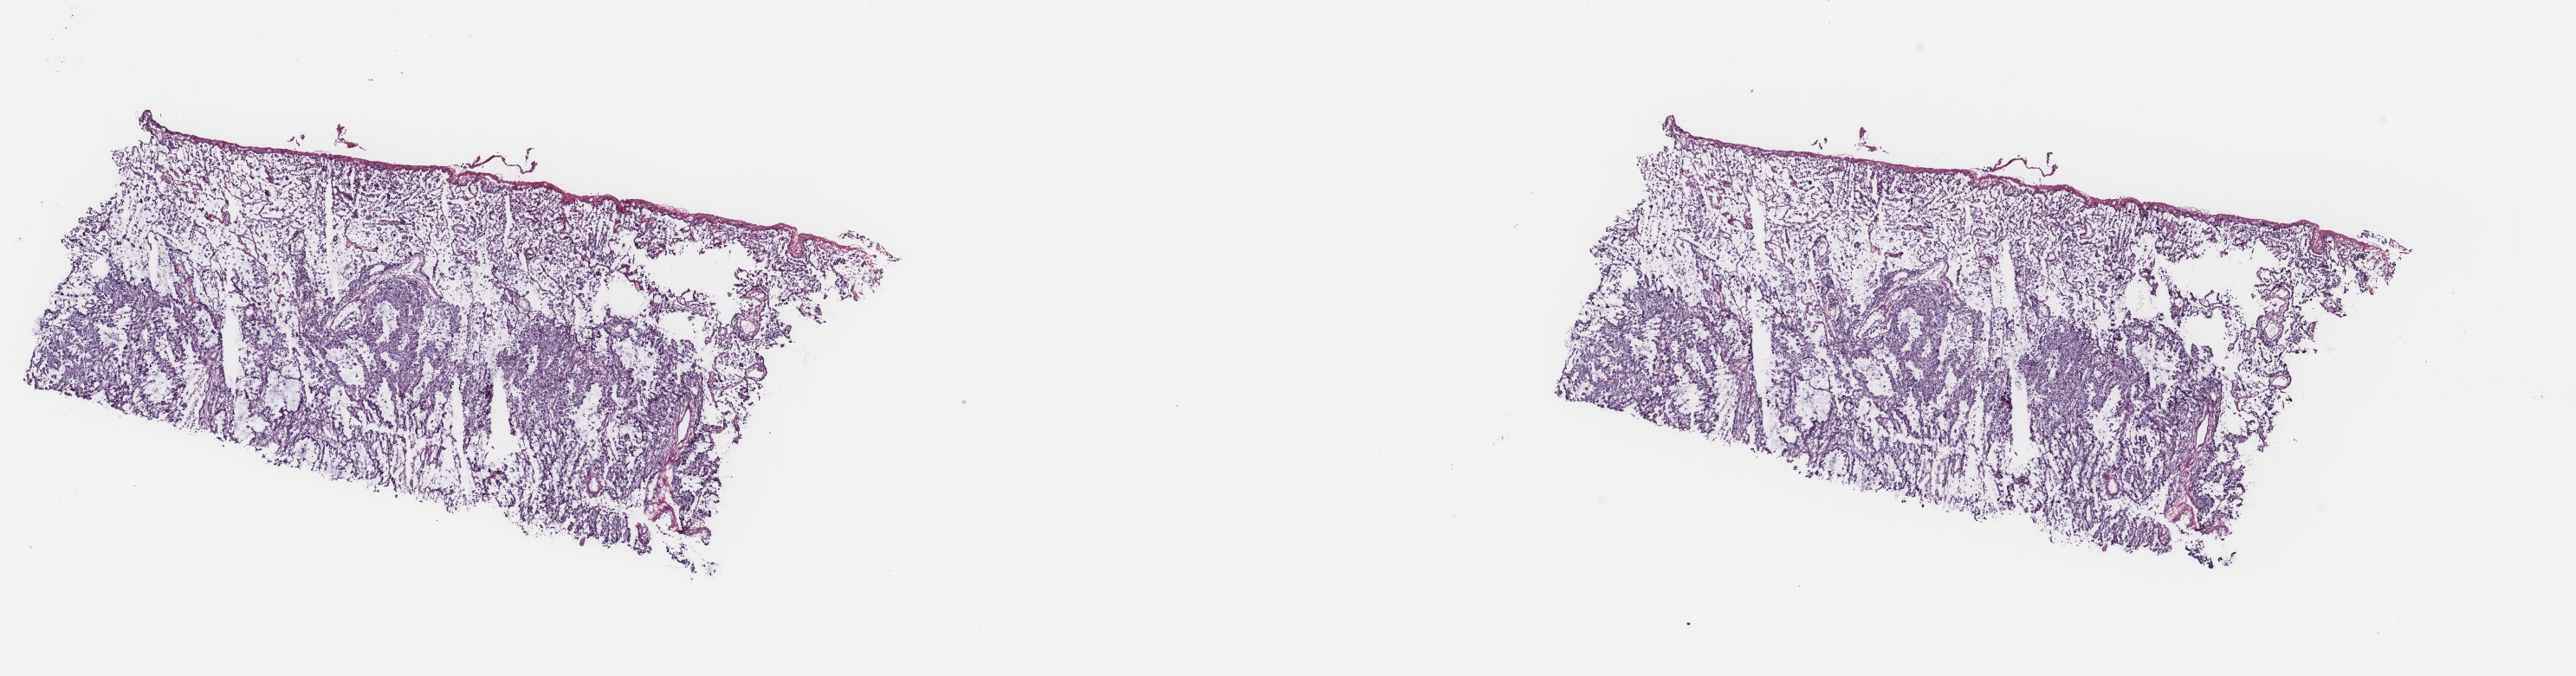
Digitized H&E tissue section (whole slide), a low-resolution overview of the entire scanned area, about 23.6 x 6.2 mm; frozen section from the top of the tissue portion; lung, primary tumour sample. Female patient; age at initial diagnosis 75 years. Pathologist review of this section (percent, as recorded): tumour cells 100%, tumour nuclei 65%, normal cells 0%, stromal cells 0%, necrosis 0%. Inflammatory infiltration, as recorded: lymphocyte infiltration 0%, monocyte infiltration 0%, neutrophil infiltration 0%.
Diagnosis: Adenocarcinoma, NOS (lower lobe, lung). AJCC pathologic stage: IV.